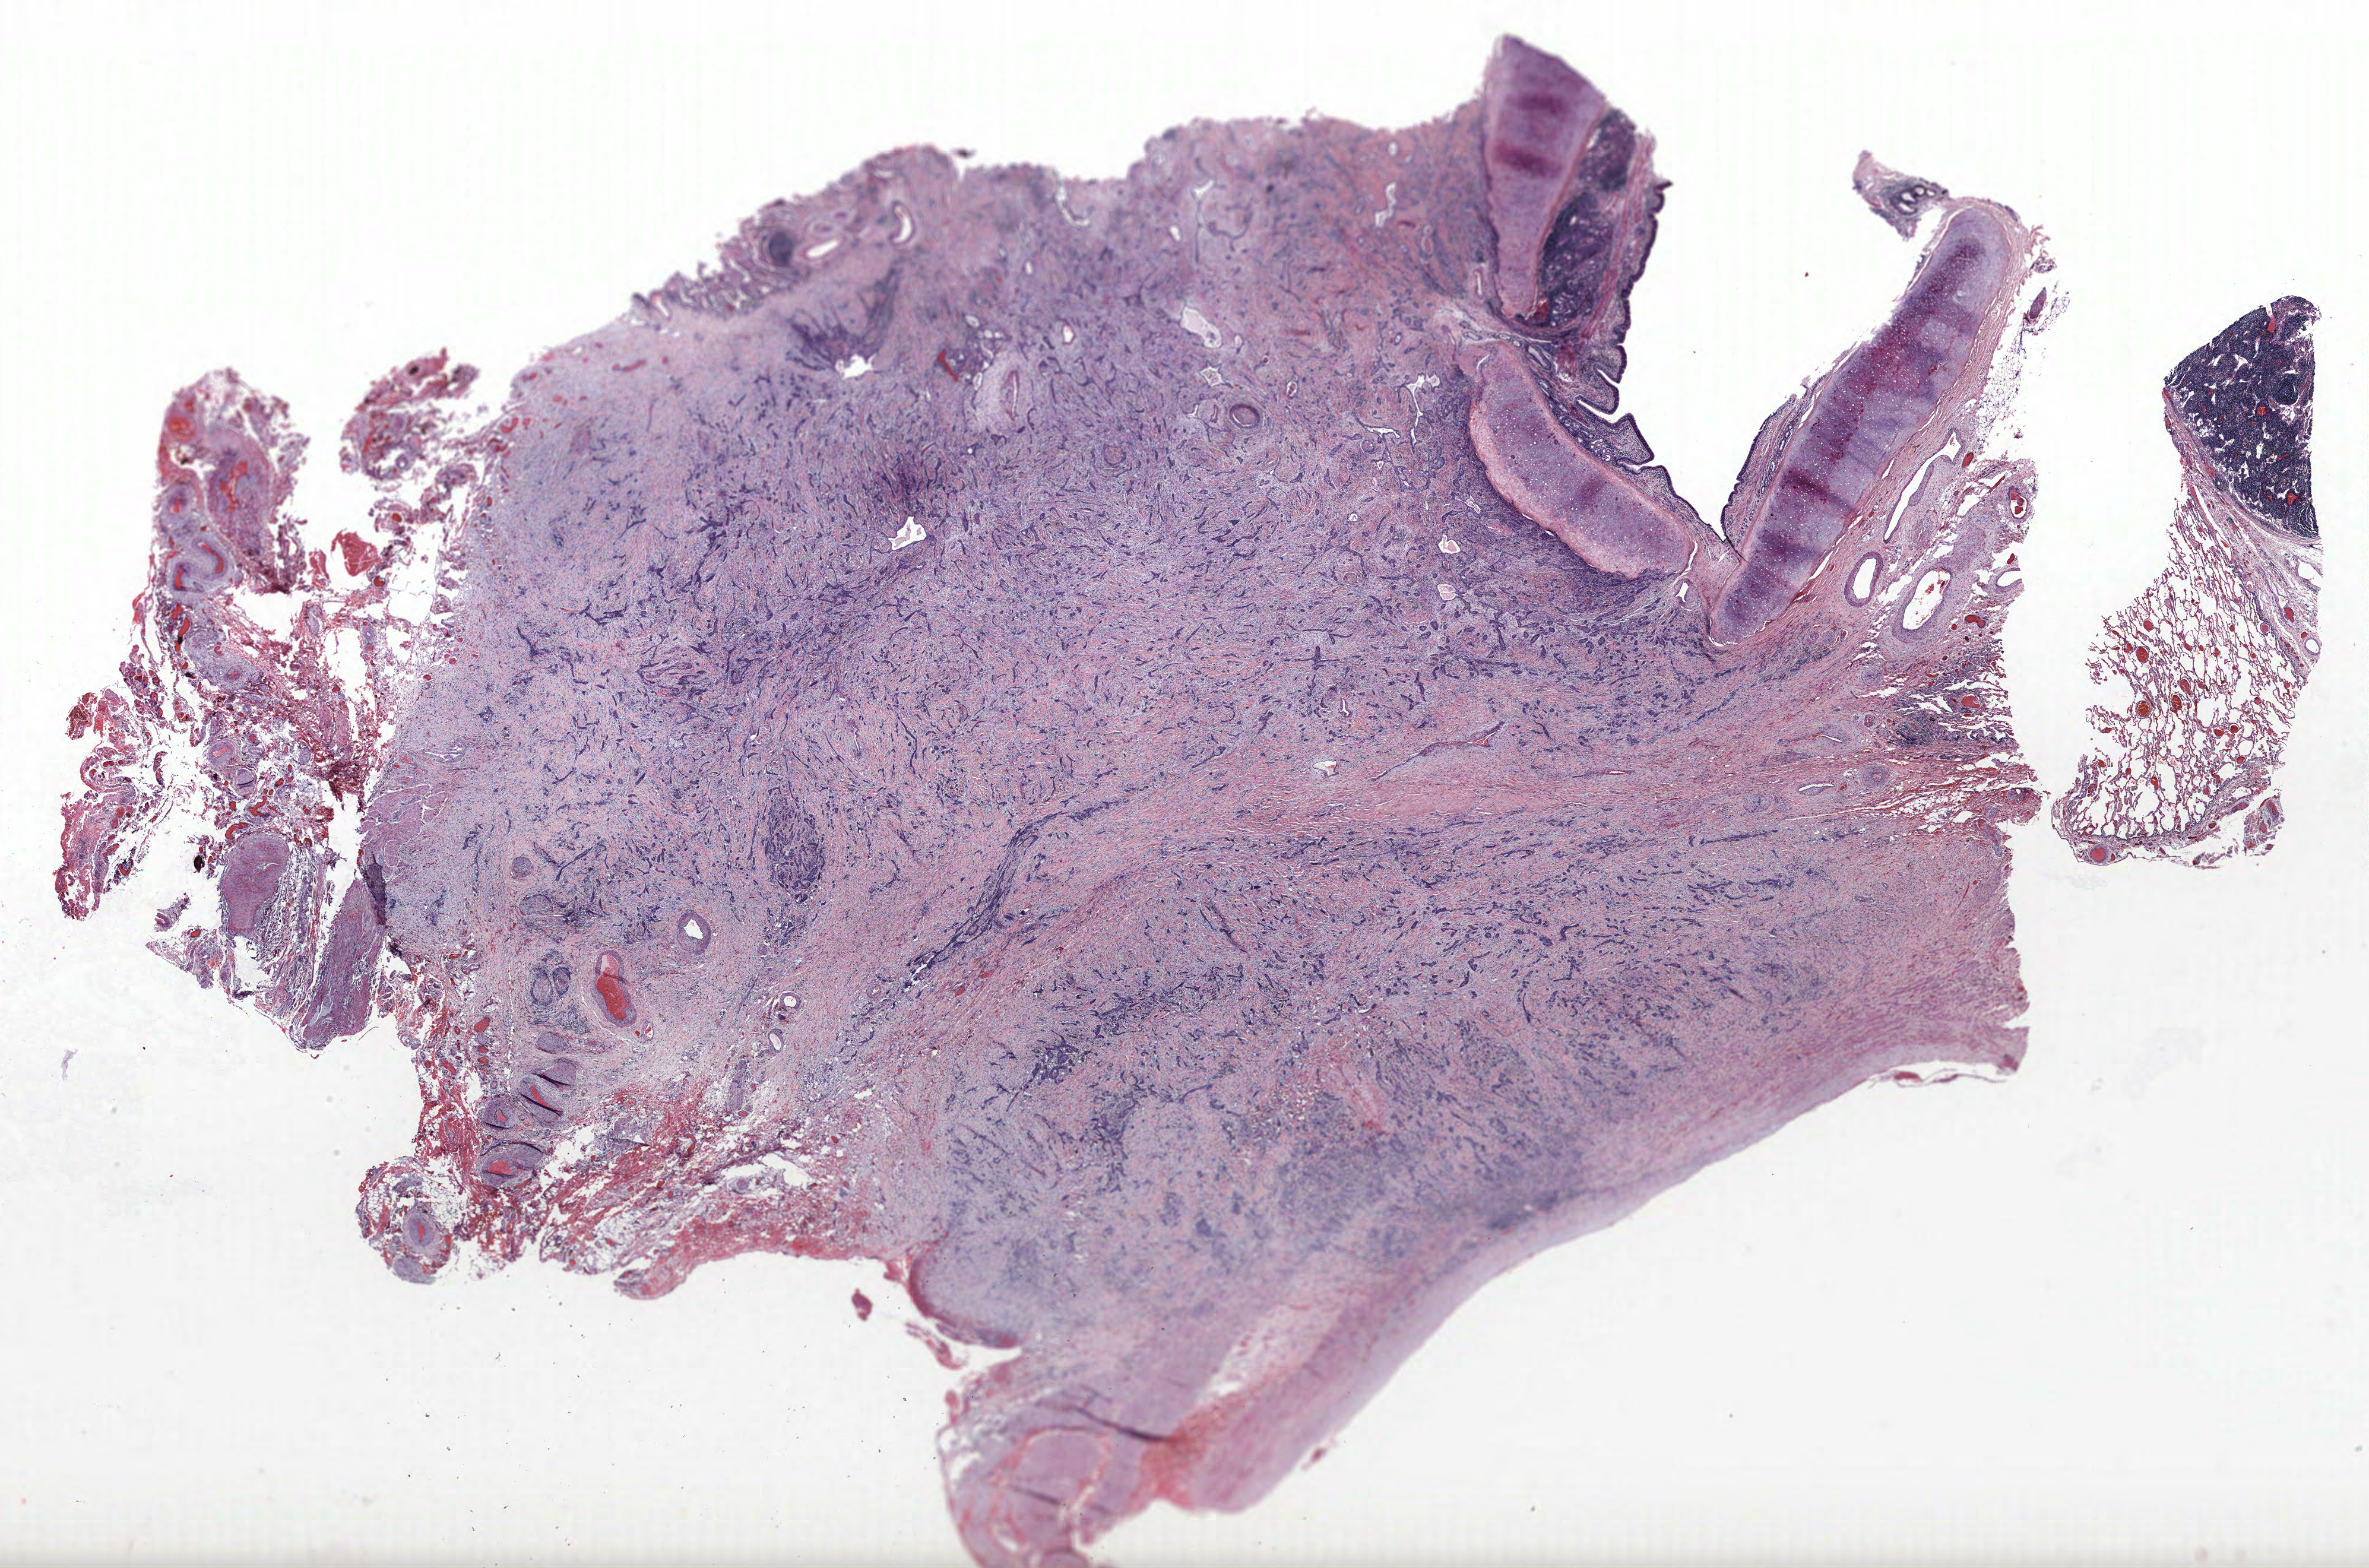
Whole-slide histology image, H&E — whole scanned area (about 31.9 x 21.1 mm) shown as a low-resolution overview. Formalin-fixed paraffin-embedded (FFPE) section. Lung. Female patient, aged 62 at enrolment. Grade: poorly differentiated (G3).
Primary tumour location (clinical record): left hilum. Tumour size (pathology): 50 mm. Stage (AJCC 6th edition): IIIB. Participant's lung-cancer diagnosis: Squamous cell carcinoma, NOS (ICD-O-3 8070/3).